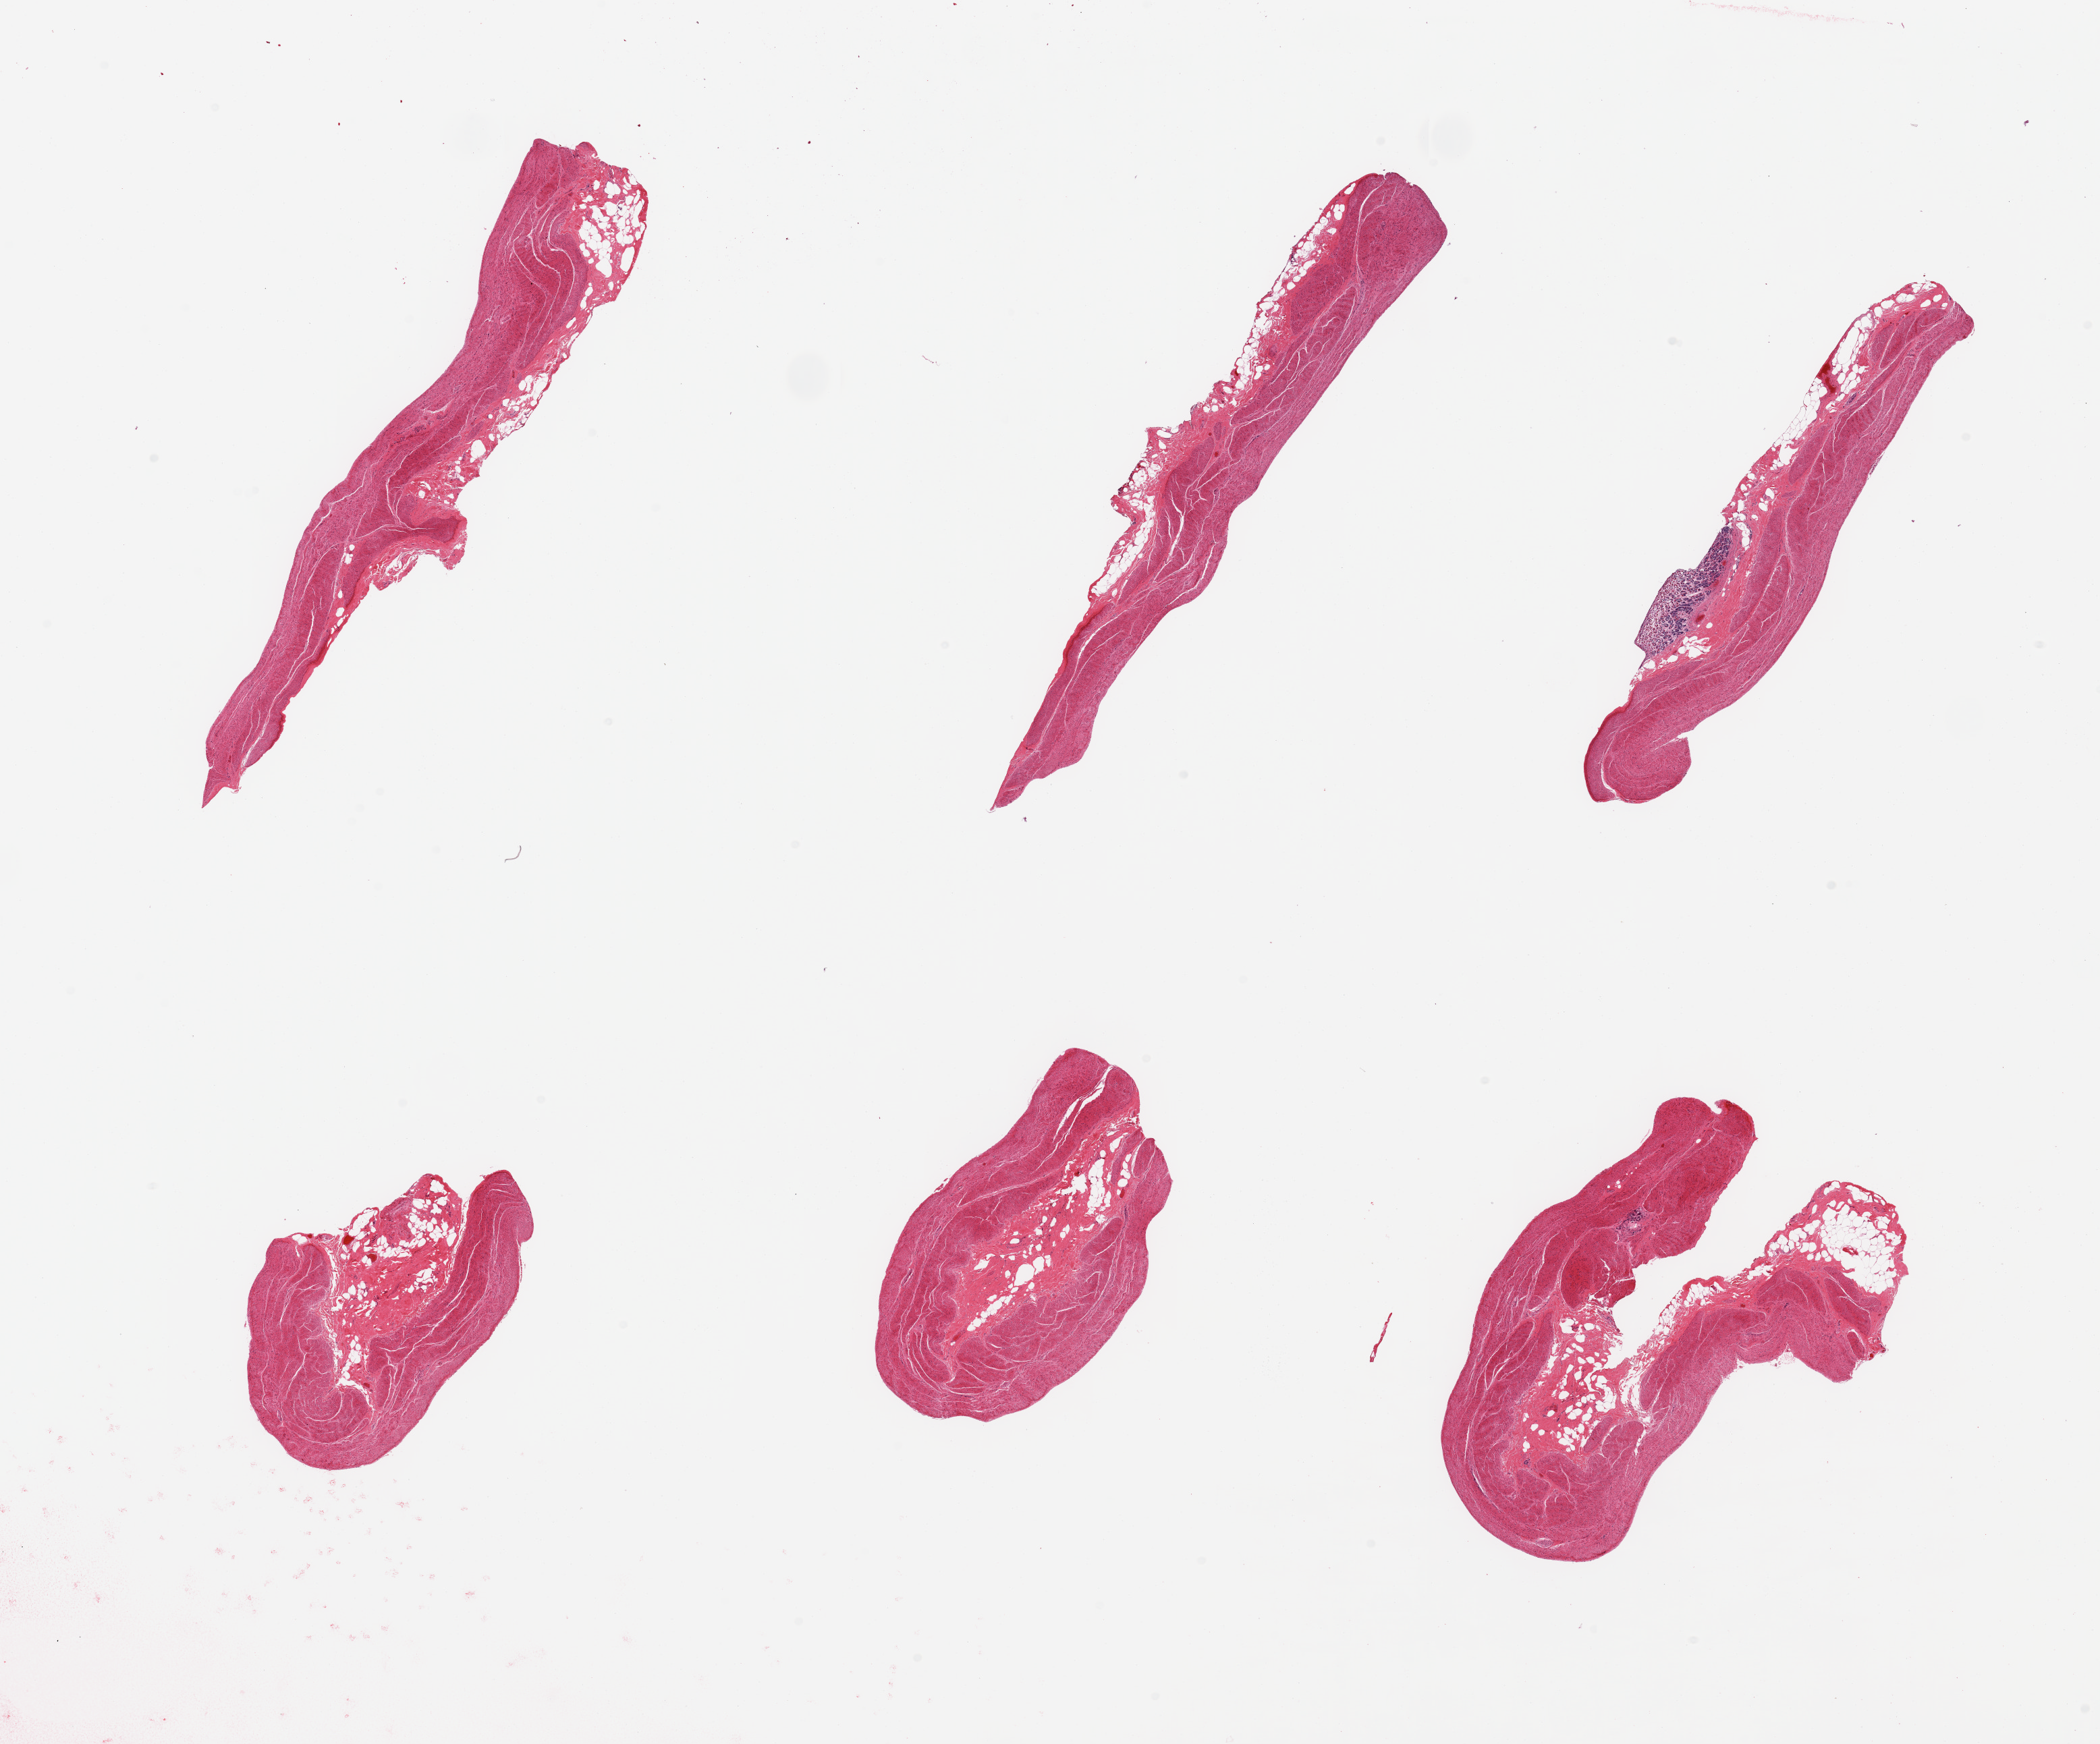
Whole-slide image, hematoxylin and eosin (H&E) stain, low-resolution overview of the scanned area, about 24.6 x 20.4 mm, PAXgene-fixed paraffin-embedded (PFPE) section, target tissue: stomach, donor tissue sample. Donor sex: male.
Review note (as recorded): 6 pieces; predominantly muscularis, only 1 piece includes a small strip of mucosa.